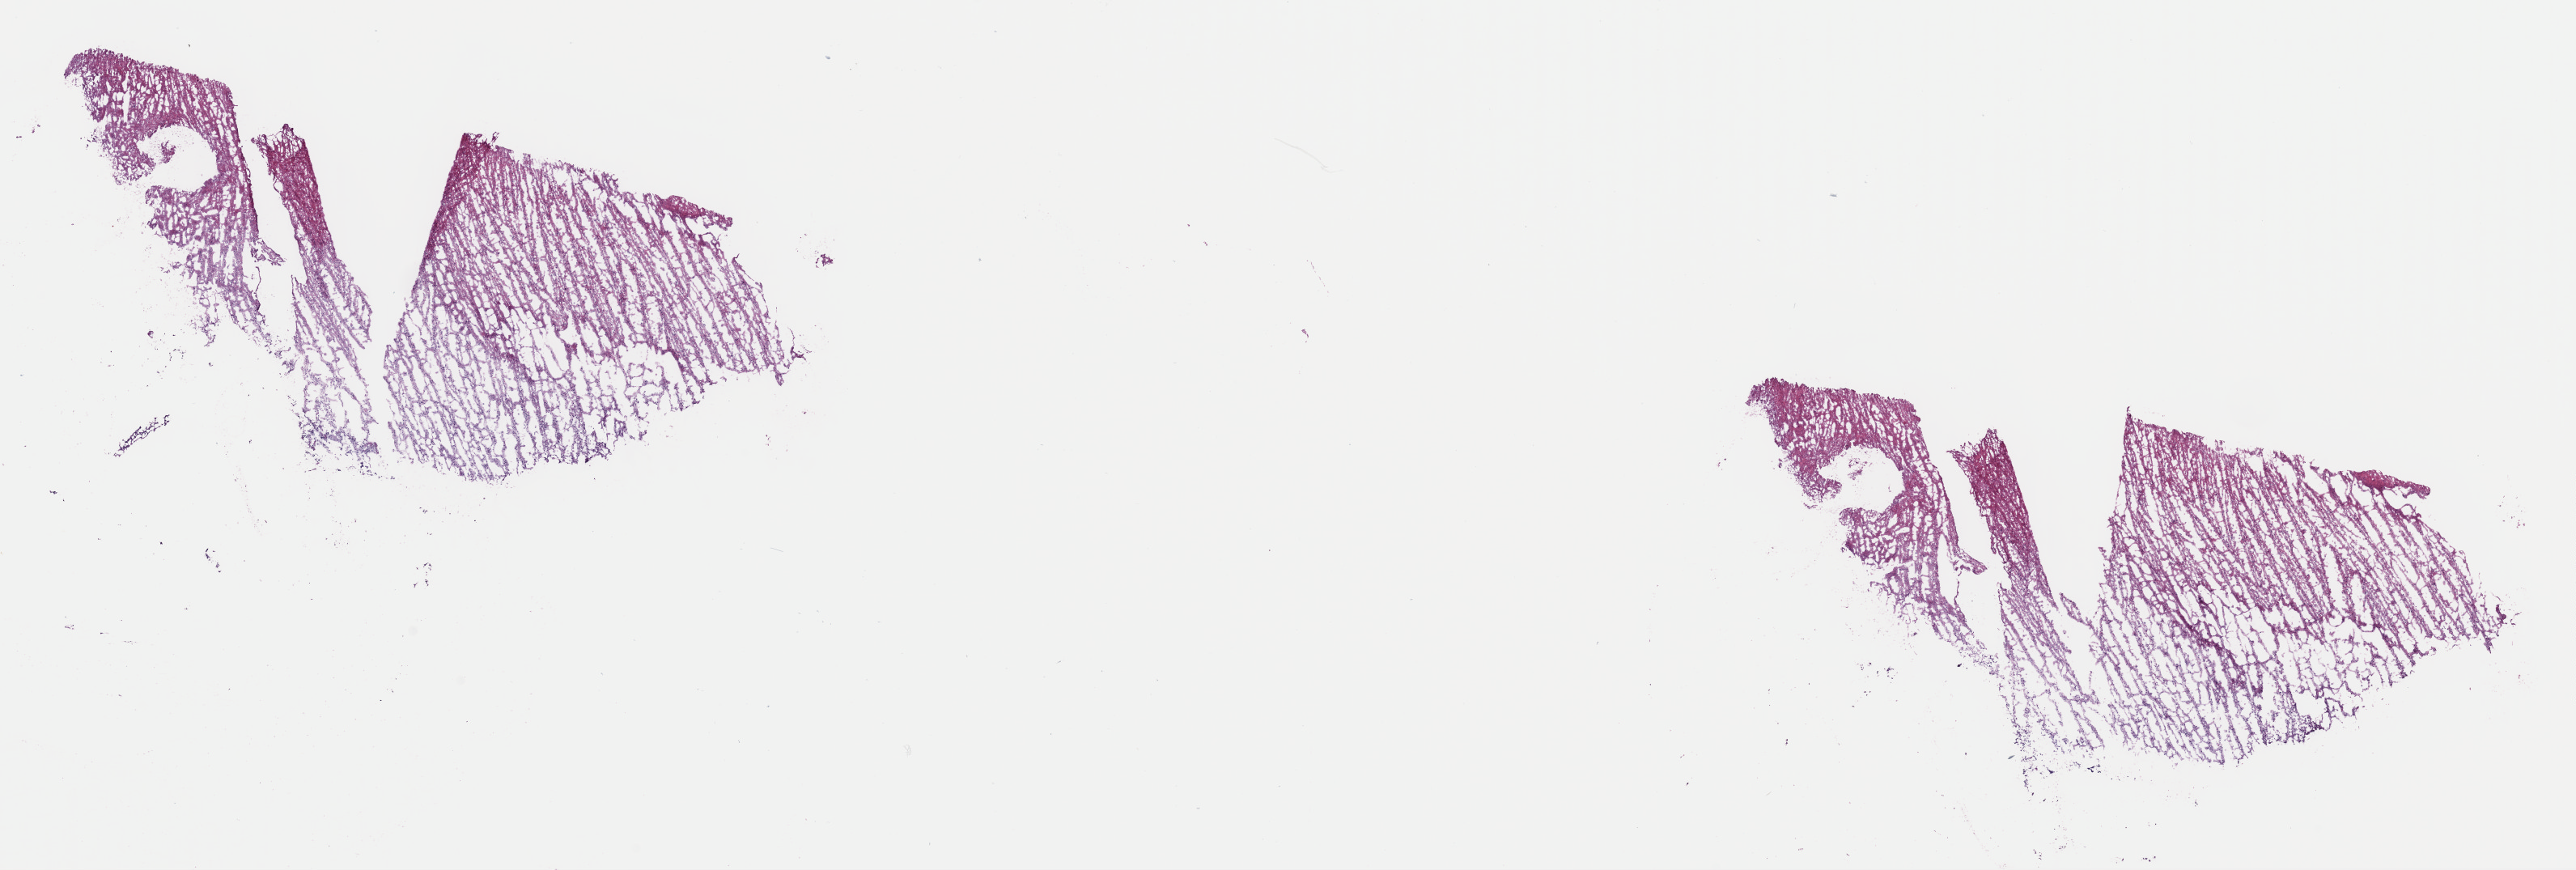
Digitized Hematoxylin and eosin (H&E) stained tissue section (whole slide) — low-resolution overview of the scanned area, about 25.1 x 8.5 mm, frozen section from the top of the tissue portion, brain, primary tumour sample. Female, age 37 years at initial diagnosis. Histologic grade: G3 (poorly differentiated). Slide review estimates, as recorded: tumour cells 50%, tumour nuclei 70%, normal cells 10%, stromal cells 40%, necrosis 0%. Infiltration values recorded for this section: lymphocyte infiltration 0%, monocyte infiltration 0%, neutrophil infiltration 0%.
Histologic diagnosis: Mixed glioma.